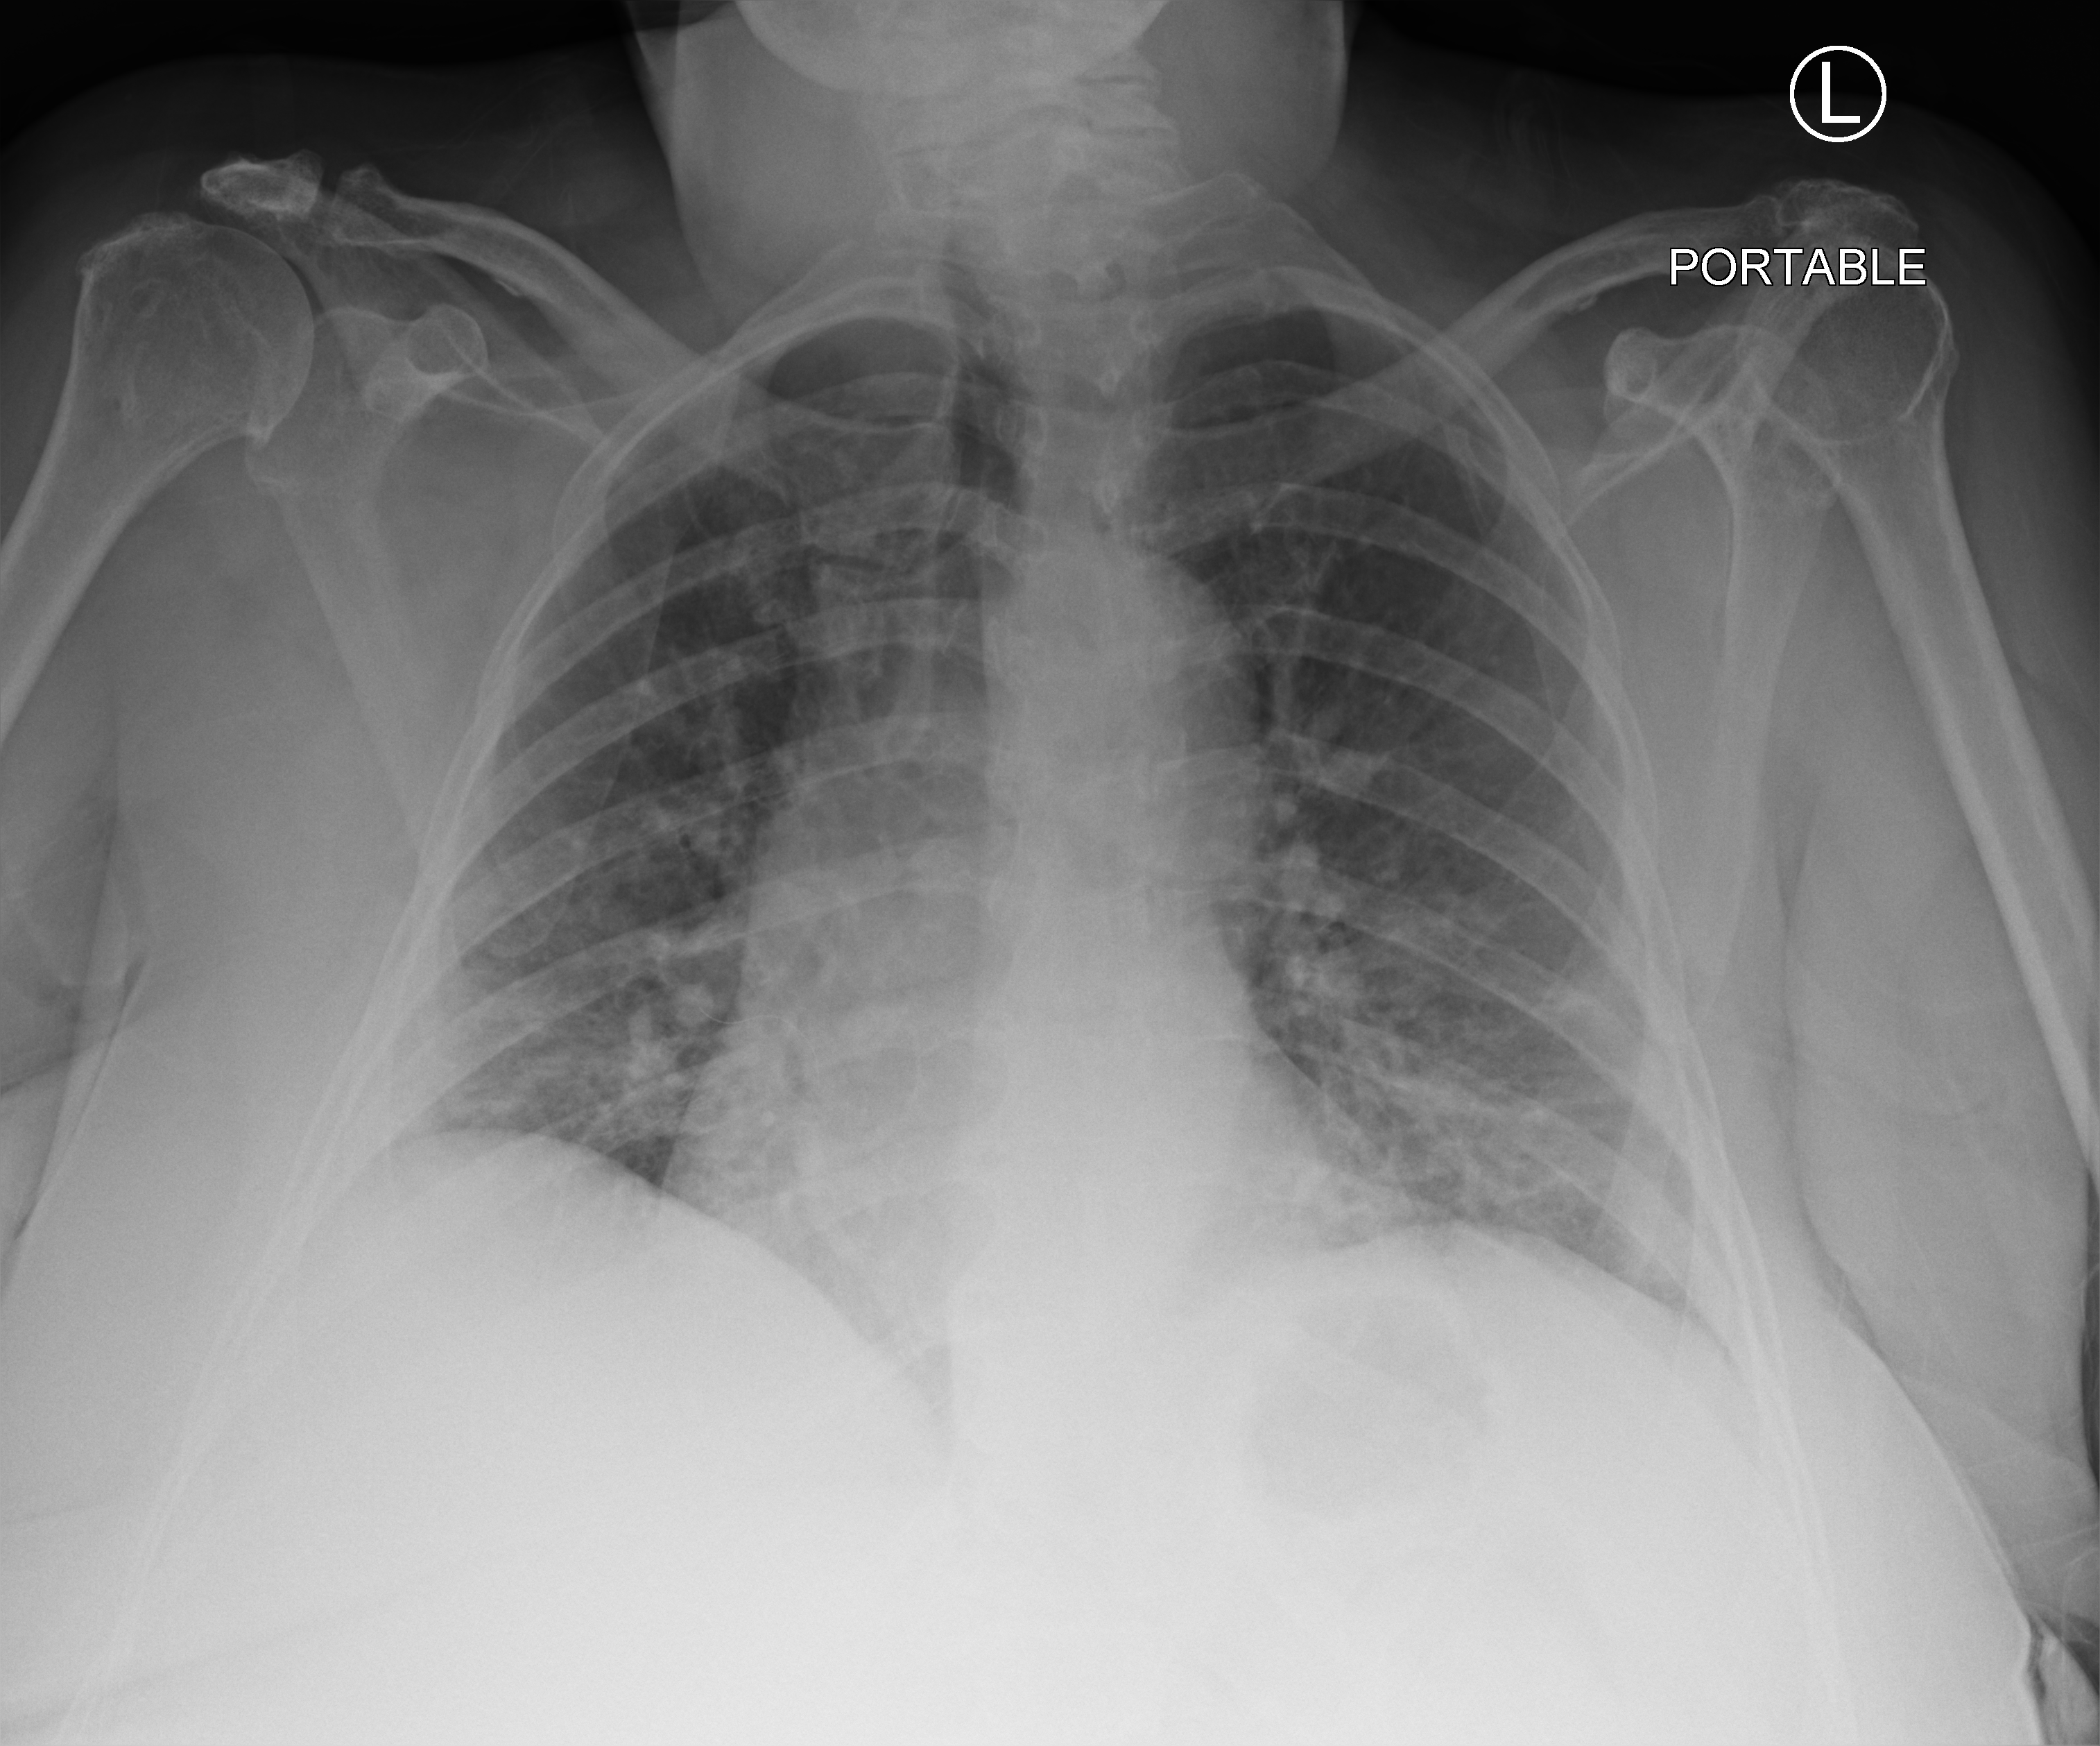
Chest X-ray (portable), anteroposterior (AP) projection. Female patient hospitalised with COVID-19, age 60–74 years.
Admission-level facts for this patient (not findings on this image; timing relative to this image not recorded): length of hospital stay: 10 days.